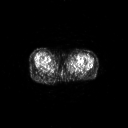
FDG PET of an extremity soft-tissue mass (from a PET/CT study), one axial slice. Slice 58 of 91 in the series (ordered by position). 3.27 mm slice thickness. 128 × 128 image matrix, field of view 700 × 700 mm. Patient: female, 74 years. Case-level facts recorded for this patient, not image findings: histological type: pleomorphic leiomyosarcoma; grade: high; site of the primary tumour: left thigh.
Structures marked on this image (expert contour drawn on MRI and transferred to this co-registered scan by the dataset authors):
- gross tumour volume including surrounding oedema: bounding box [x1, y1, x2, y2] px = [68, 56, 72, 58]